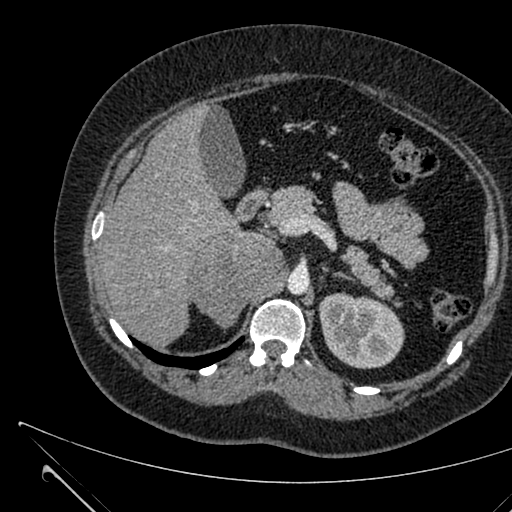
Contrast-enhanced abdominal CT, one axial slice. Slice 420 of 731 in the series (ordered by position). 120 kVp. Intravenous contrast given. Soft-tissue window (W 400 / L 40 HU). 512 × 512 image matrix. Patient: female, 36 years. From the clinical record (not read from this slice): diagnosis: adrenocortical carcinoma; tumour side: right adrenal; tumour size at pathology: 10 cm; Ki-67 index: 20 %; stage (as recorded): 4.
Outlined on this slice (semi-automatic segmentation, software-assisted and operator-edited):
- mass: bounding box <190,233,284,325> (left, top, right, bottom; pixels)